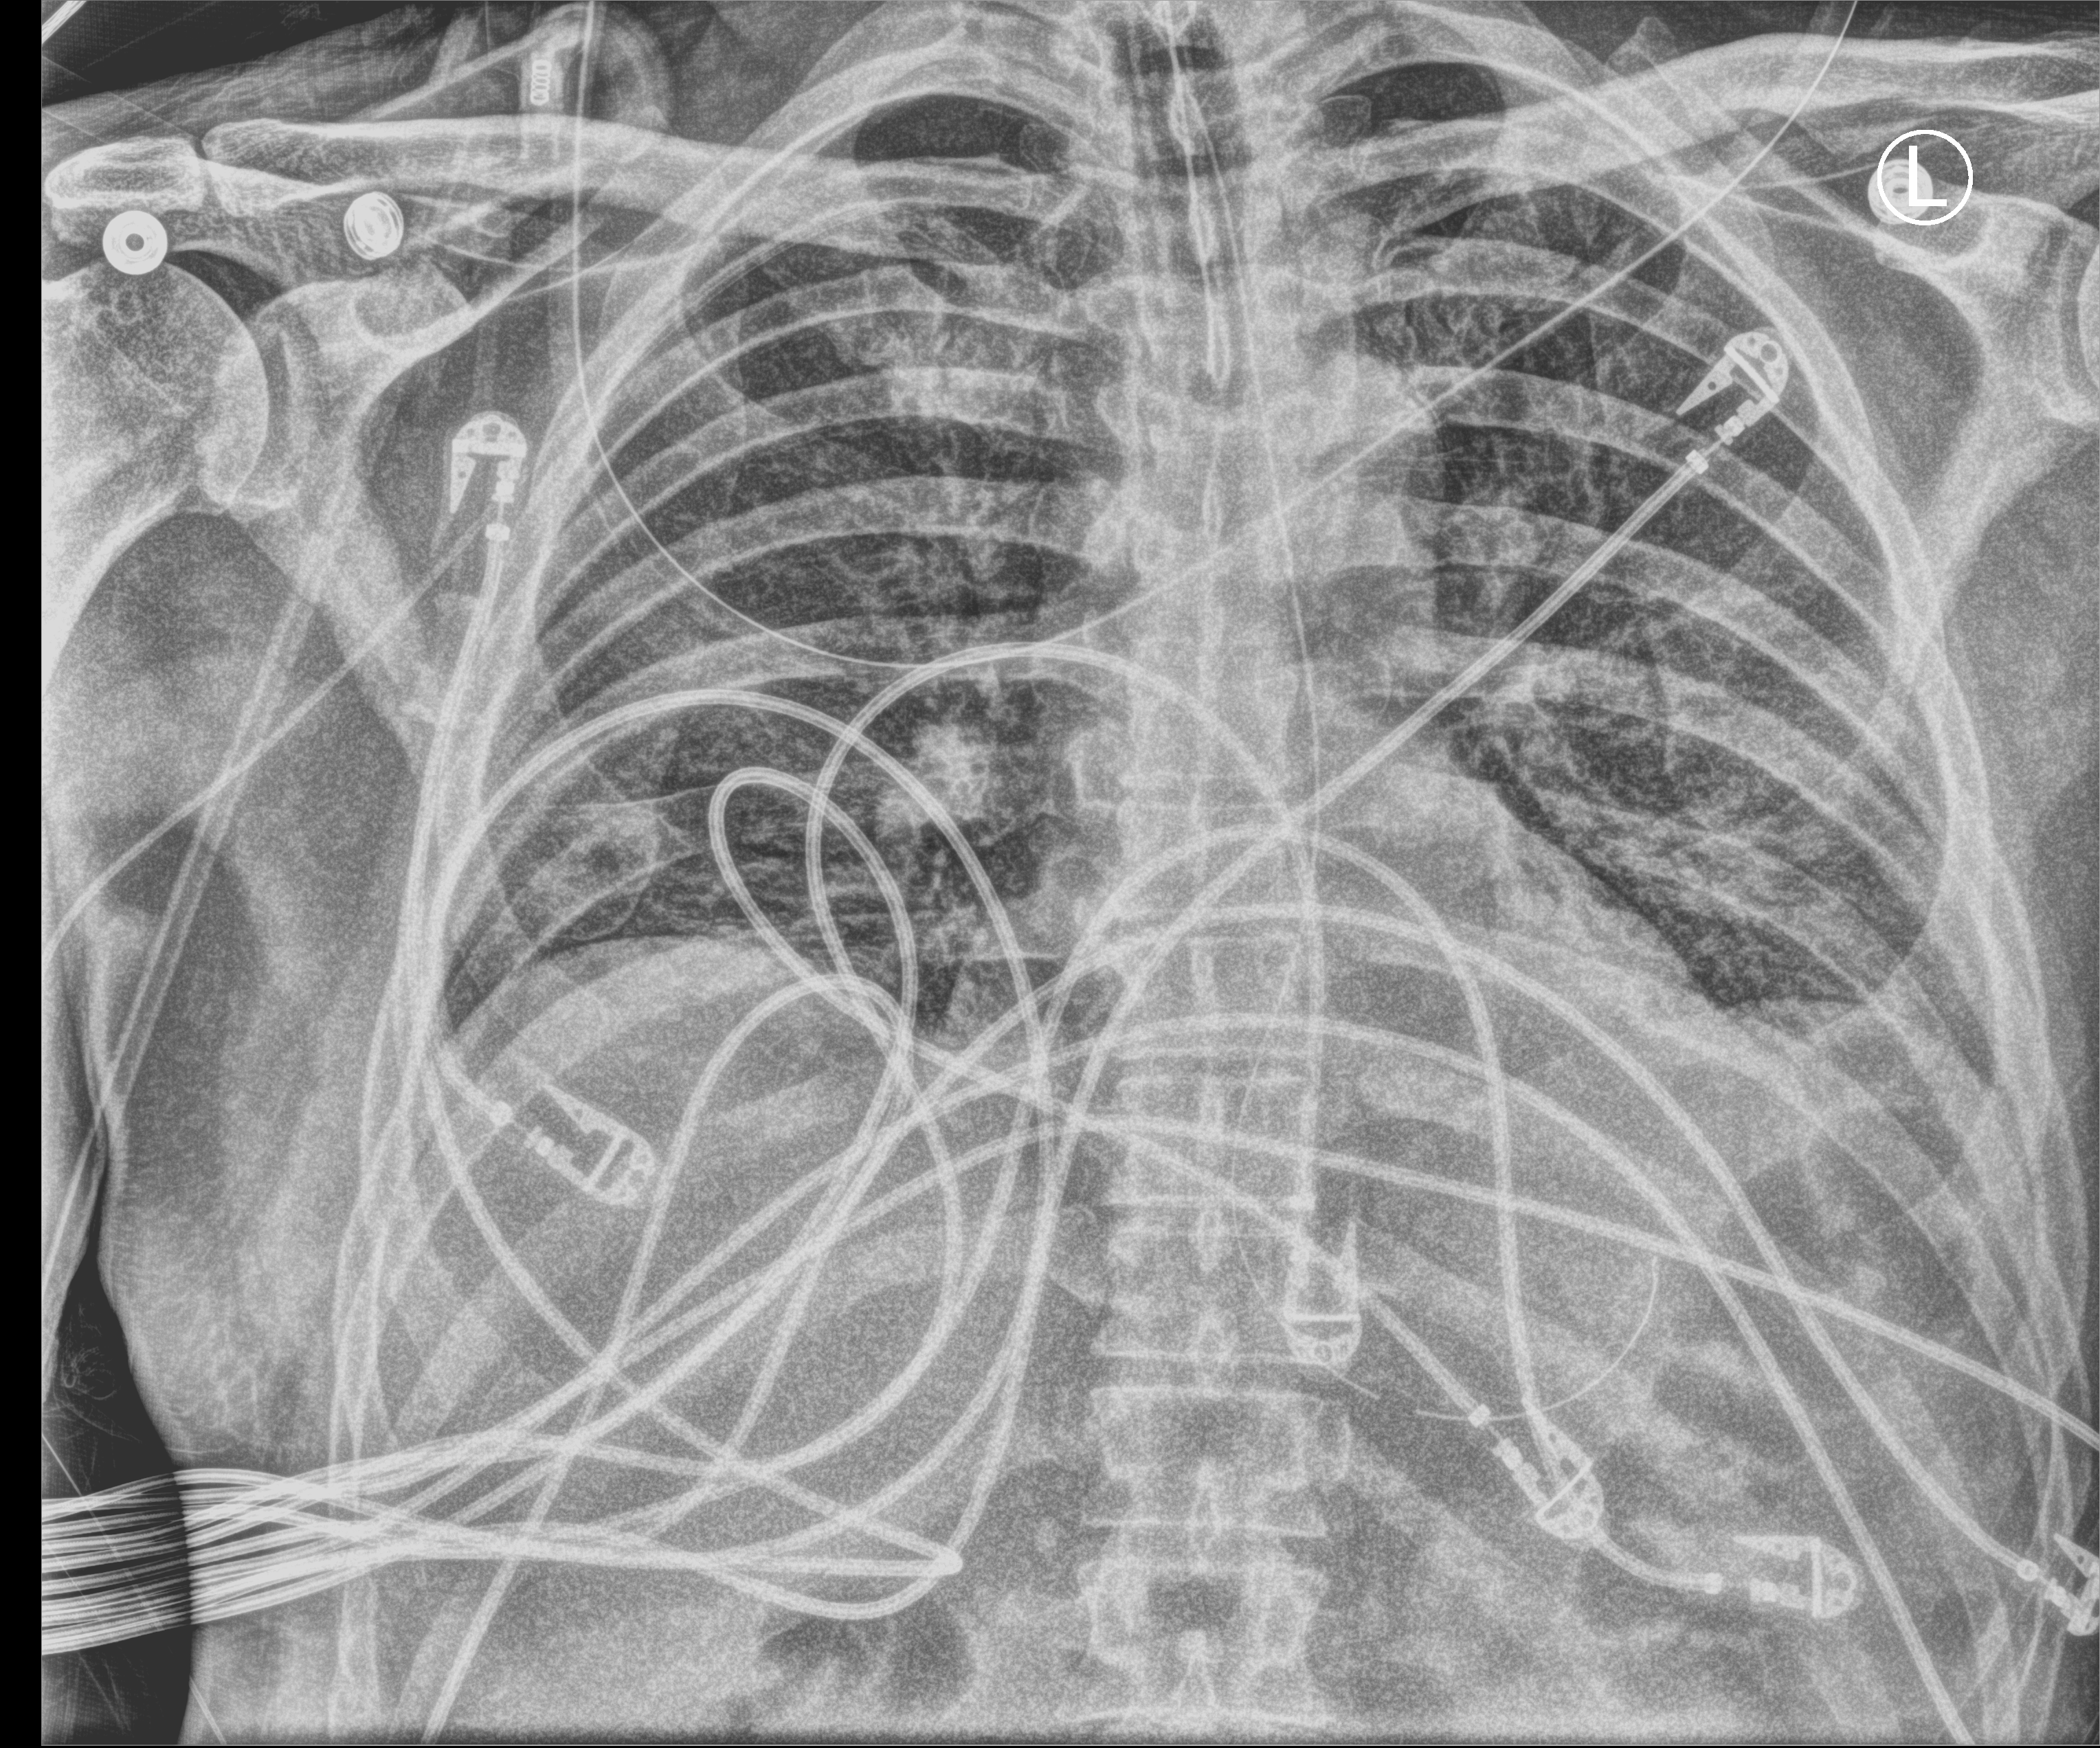
Chest X-ray (portable), anteroposterior (AP) projection. Male patient hospitalised with COVID-19, age 60–74 years.
From the hospital-stay record, not from the radiograph (when in the stay this image was taken is not recorded): mechanically ventilated during this hospital stay: yes; length of hospital stay: 26 days; chronic kidney disease (admission record): no.